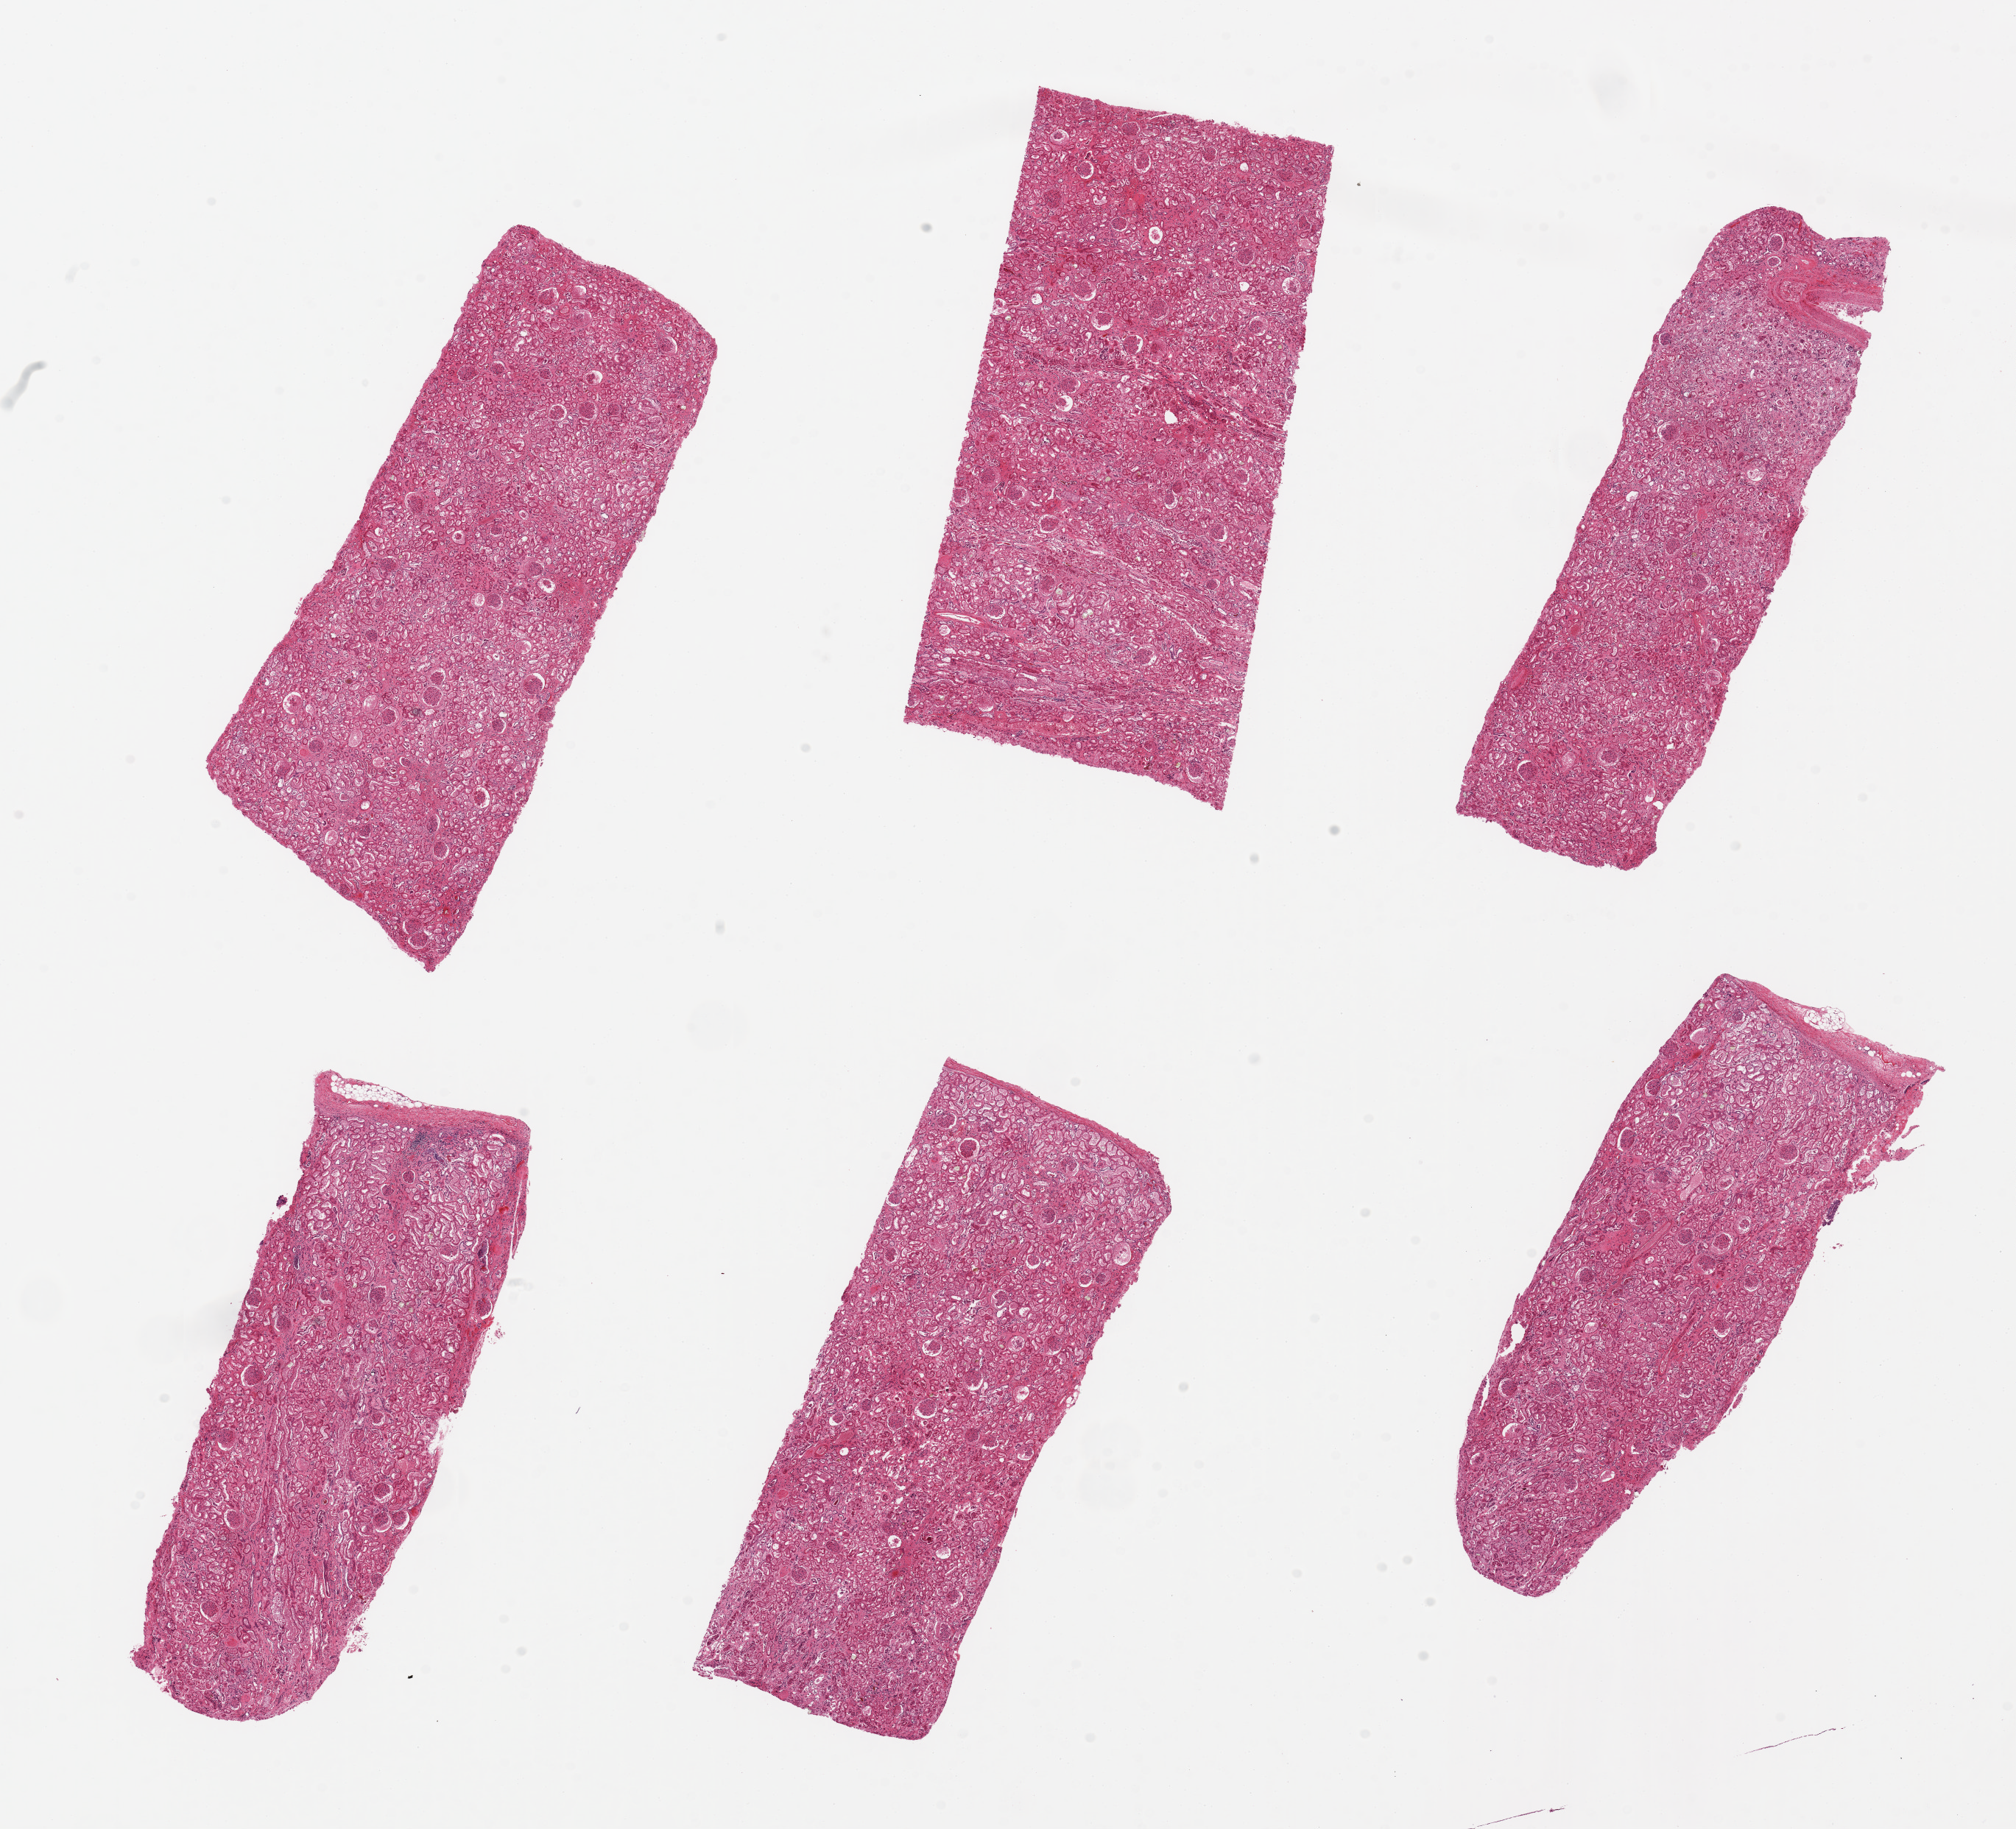
Hematoxylin and eosin (H&E) whole-slide image — a low-resolution overview of the entire scanned area, about 21.7 x 19.6 mm (slide scanned at 20x), PAXgene-fixed paraffin-embedded (PFPE) section, sampled site (target tissue): renal cortex, tissue donor sample. Donor sex: male.
• review note (as recorded): 6 pieces, up to 7x3mm; cortex with crystals in tubules; little sclerosis